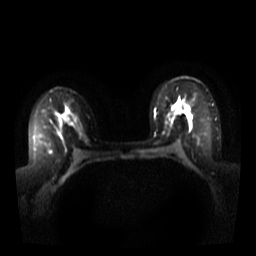
Breast MRI, one axial slice. Slice 20 of 44 in the series (ordered by position). Diffusion-weighted series; image 2 of 4 stored at this slice position (different b-values; order by instance number). 3 T. 5 mm slice thickness. 256 × 256 image matrix, field of view 340 × 340 mm. Female patient.
Structures marked on this image (outlined manually by an expert reader):
- tumour on diffusion-weighted imaging: bounding box [x1, y1, x2, y2] px = [186, 108, 189, 114]